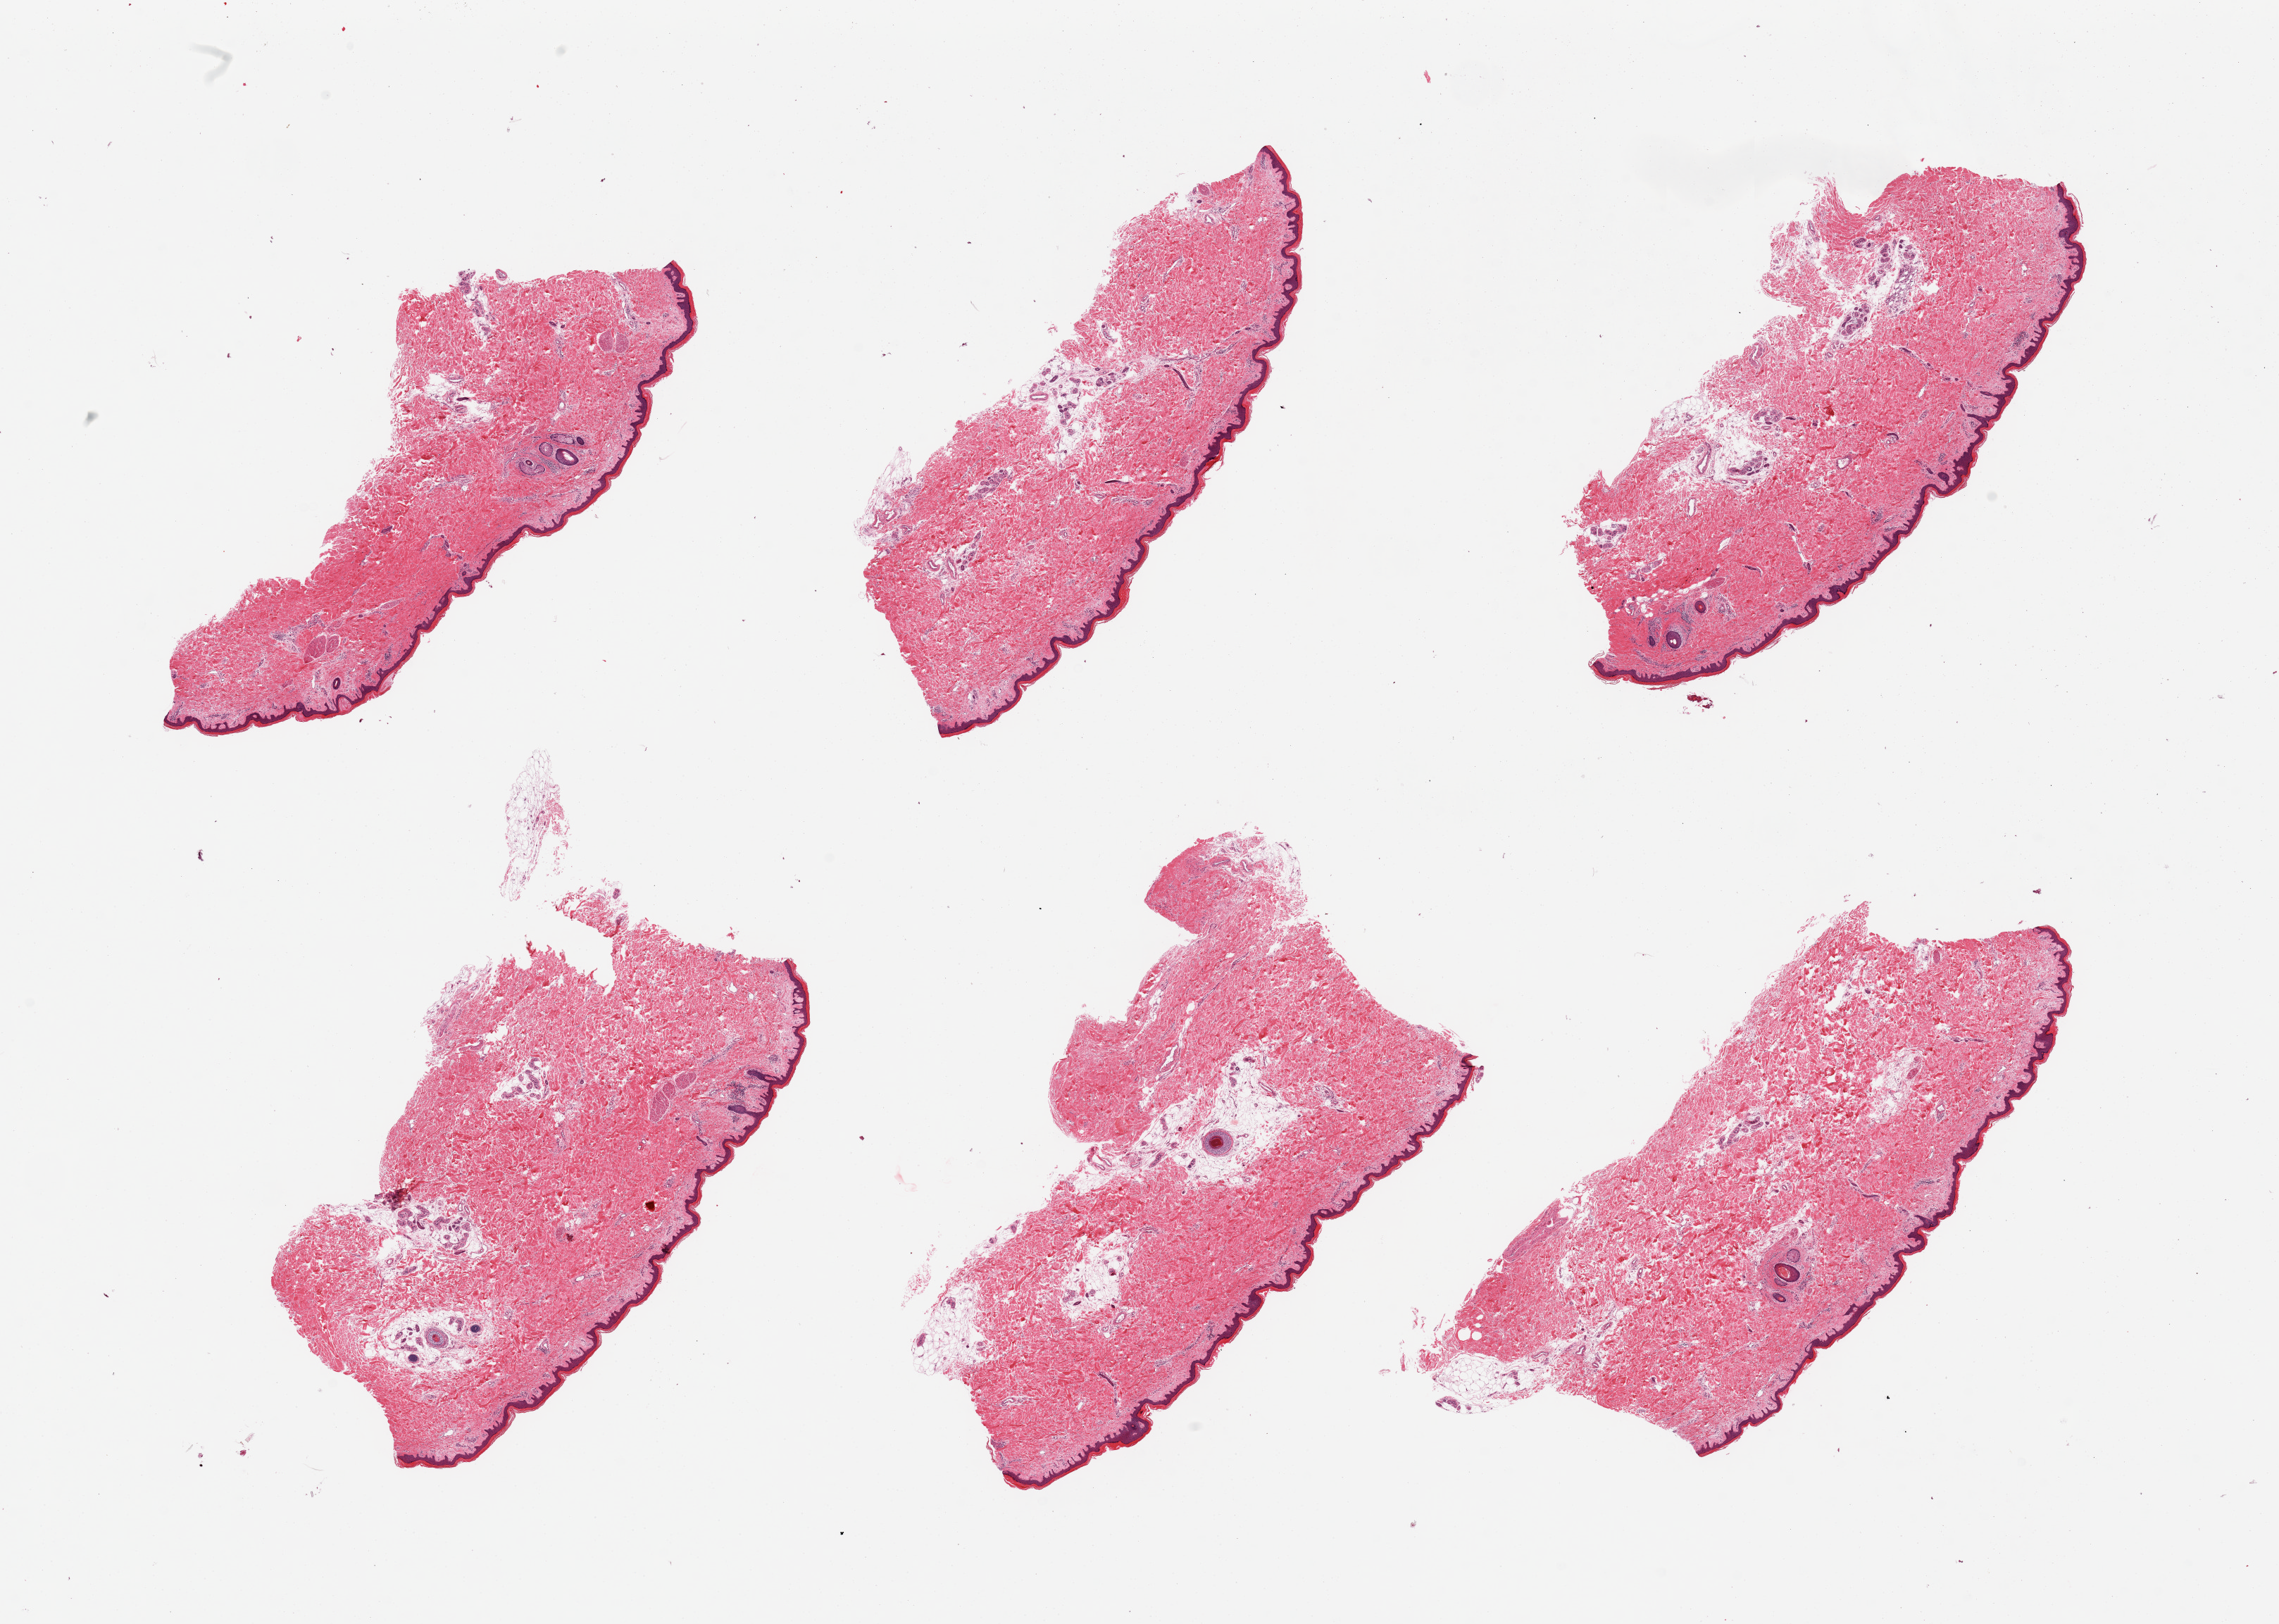
Digitized hematoxylin and eosin (H&E)-stained section, brightfield — a low-resolution overview of the entire scanned area, about 25.6 x 18.2 mm (from a 20x scan); PAXgene-fixed paraffin-embedded (PFPE) section; sampled site (target tissue): skin of lower leg; donor tissue sample. Donor: female.
Pathologist's review note for this sample: 6 pieces, minimal adherent fat.